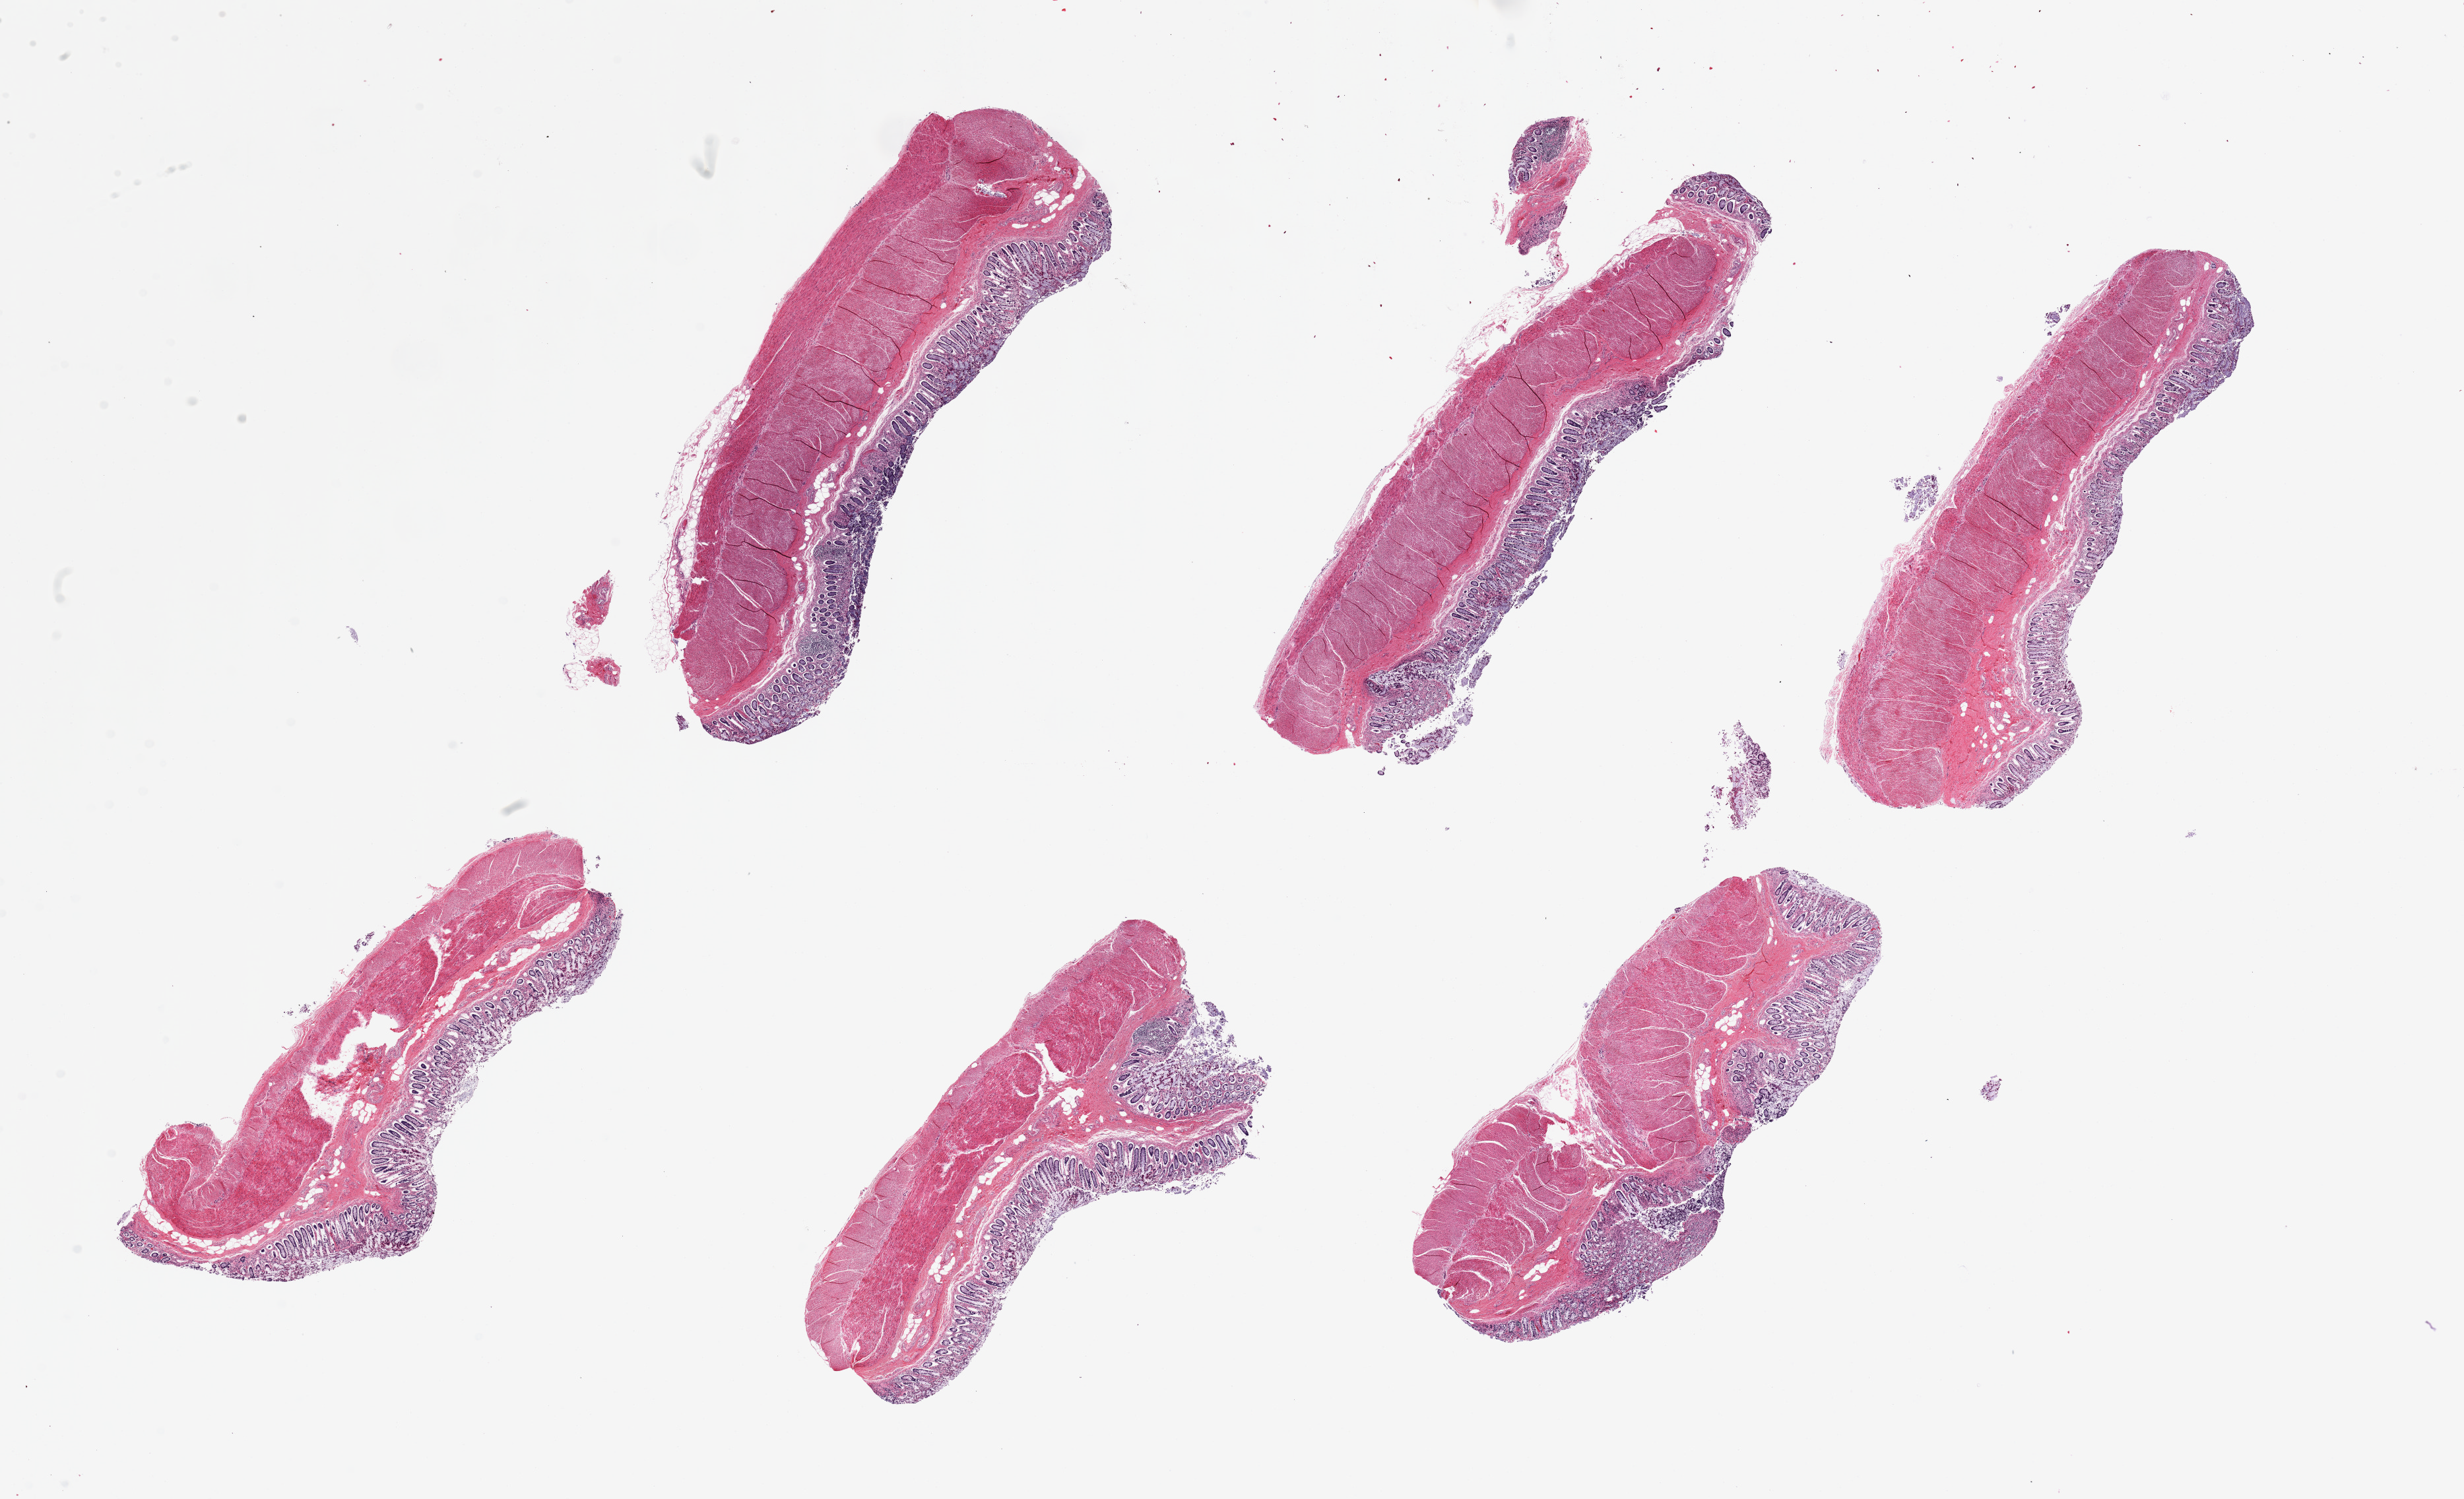
Digitized H&E-stained section, brightfield — shown as a low-resolution overview of the whole scanned area (about 29.5 x 18.0 mm, from a 20x scan). PAXgene-fixed paraffin-embedded (PFPE) section. Section of transverse colon (target tissue). Donor tissue sample. Donor sex: female.
Pathologist's review note for this sample: 6 pieces ~8x2.5mm, mucosa moderately-badly autolyzed, ~10-20% thickness.